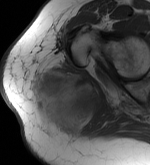
MRI of an extremity soft-tissue mass, one axial slice; slice 37 of 56 in the series (ordered by position); MR volume resampled by the dataset authors to the PET/CT grid (not the native acquisition matrix); 3.27 mm slice thickness; 150 × 165 image matrix, field of view 146 × 161 mm. Female patient. Case-level facts recorded for this patient, not image findings: histological type: epithelioid sarcoma with vascular differentiation; site of the primary tumour: right buttock.
Structures marked on this image (expert contour drawn on MRI and transferred to this co-registered scan by the dataset authors):
- gross tumour volume (mass): box from (x=28, y=69) to (x=111, y=132) px